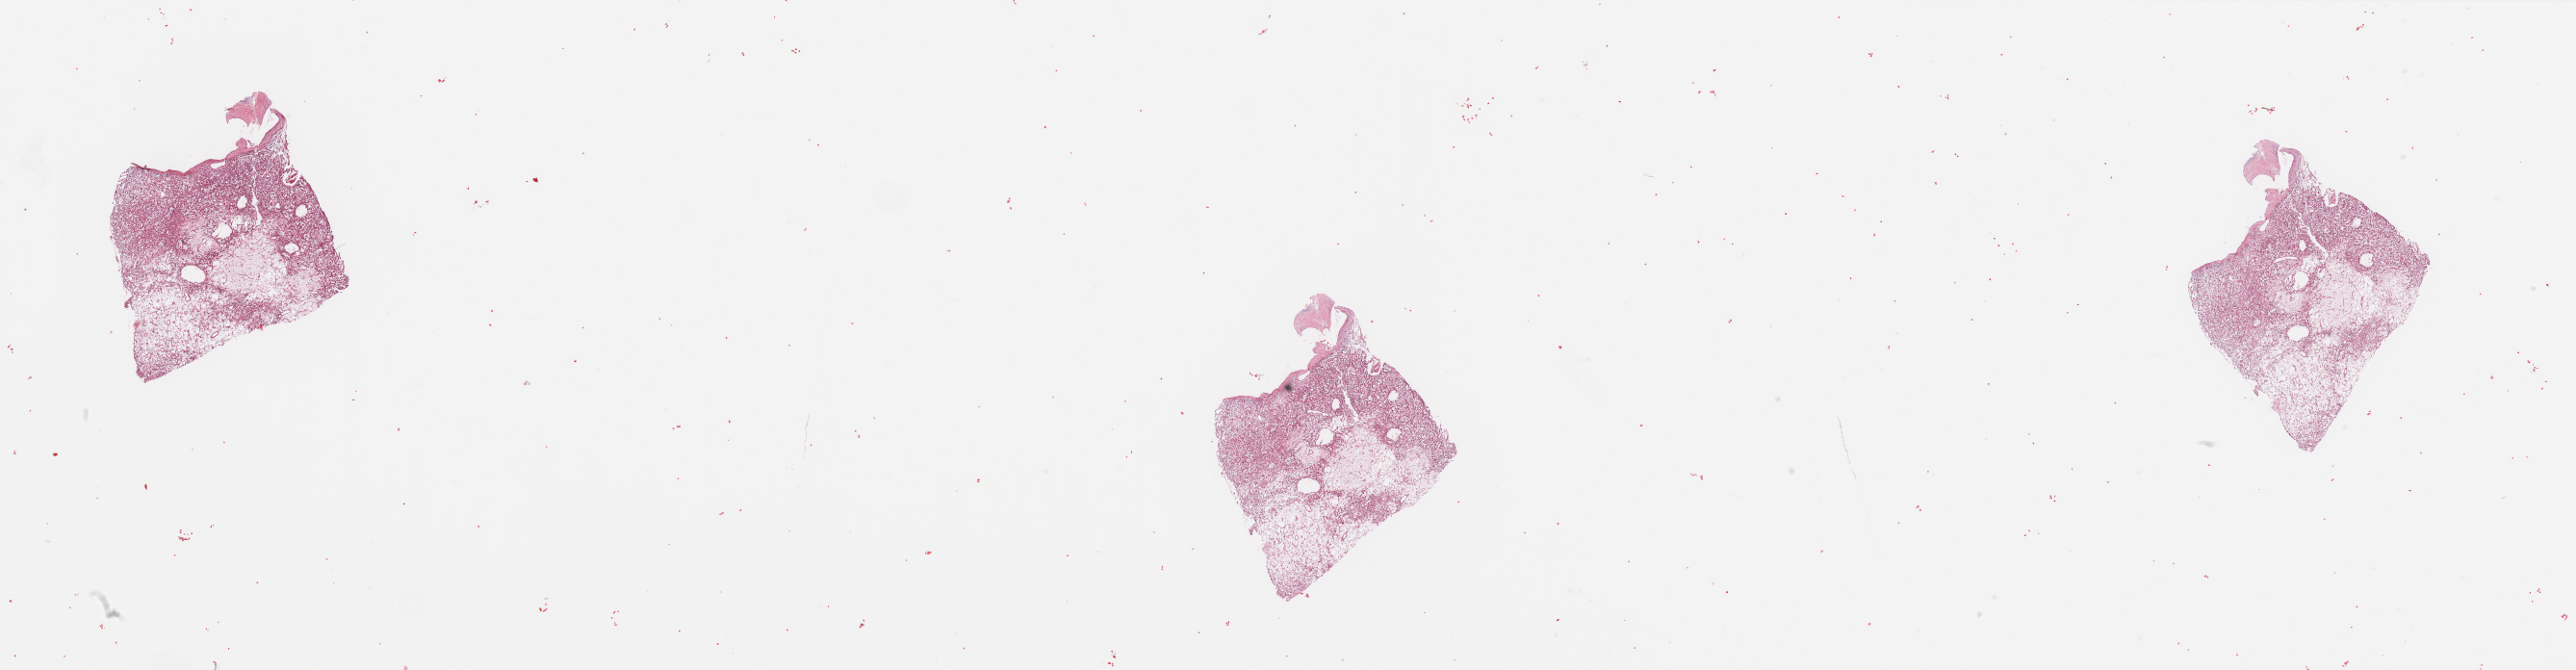
Whole-slide histology image, H&E — shown as a low-resolution overview of the whole scanned area (about 42.3 x 11.0 mm, acquisition: 20x scan). Tumour tissue sample, sampled site: kidney. Patient: male, age 68 years. Histologic grade: G1 (well differentiated). Slide review estimates, as recorded: tumour nuclei 80%, necrosis 5%.
AJCC pathologic stage: I. Diagnosis: Renal cell carcinoma, NOS. Primary tumour site (as recorded): middle.